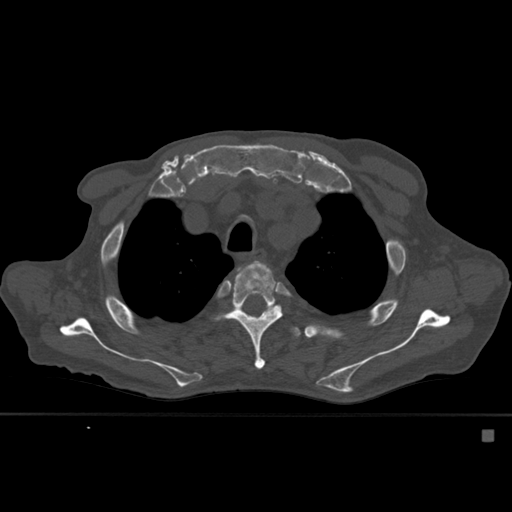
CT including the spine, one axial slice. Position 417 of 527 along the scan axis. Bone window (W 1800 / L 400 HU). 1.5 mm slice thickness. 512 × 512 image matrix. Patient: male, 78 years. From the clinical record (not read from this slice): primary cancer: prostate.
Structures marked on this image (semi-automatic segmentation, software-assisted and operator-edited):
- T3 vertebra: box from (x=235, y=264) to (x=251, y=279) px
- T4 vertebra: (x=225, y=262)–(x=285, y=370)
- T5 vertebra: (x=239, y=307)–(x=301, y=338)